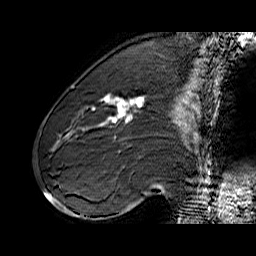
Breast MRI (dynamic contrast-enhanced), one sagittal slice; position 23 of 60 along the scan axis; dynamic contrast-enhanced series, time point 2 of 6 at this slice position (early post-contrast); 1.5 T; TE 6.4 ms, TR 32.9 ms; 4 mm slice thickness; 256 × 256 image matrix, field of view 200 × 200 mm. Female patient. From the clinical record (not read from this slice): setting: breast cancer imaged before/during neoadjuvant chemotherapy; receptor status: HER2-positive.
Structures marked on this image (semi-automatic segmentation, software-assisted and operator-edited):
- analysis volume of interest (the breast-tissue region the enhancement analysis was run in; not a lesion): box from (x=71, y=80) to (x=155, y=146) px
- tumour enhancement mask (voxels above the 100 % enhancement threshold inside the analysis volume of interest): (x=104, y=94)–(x=144, y=123)